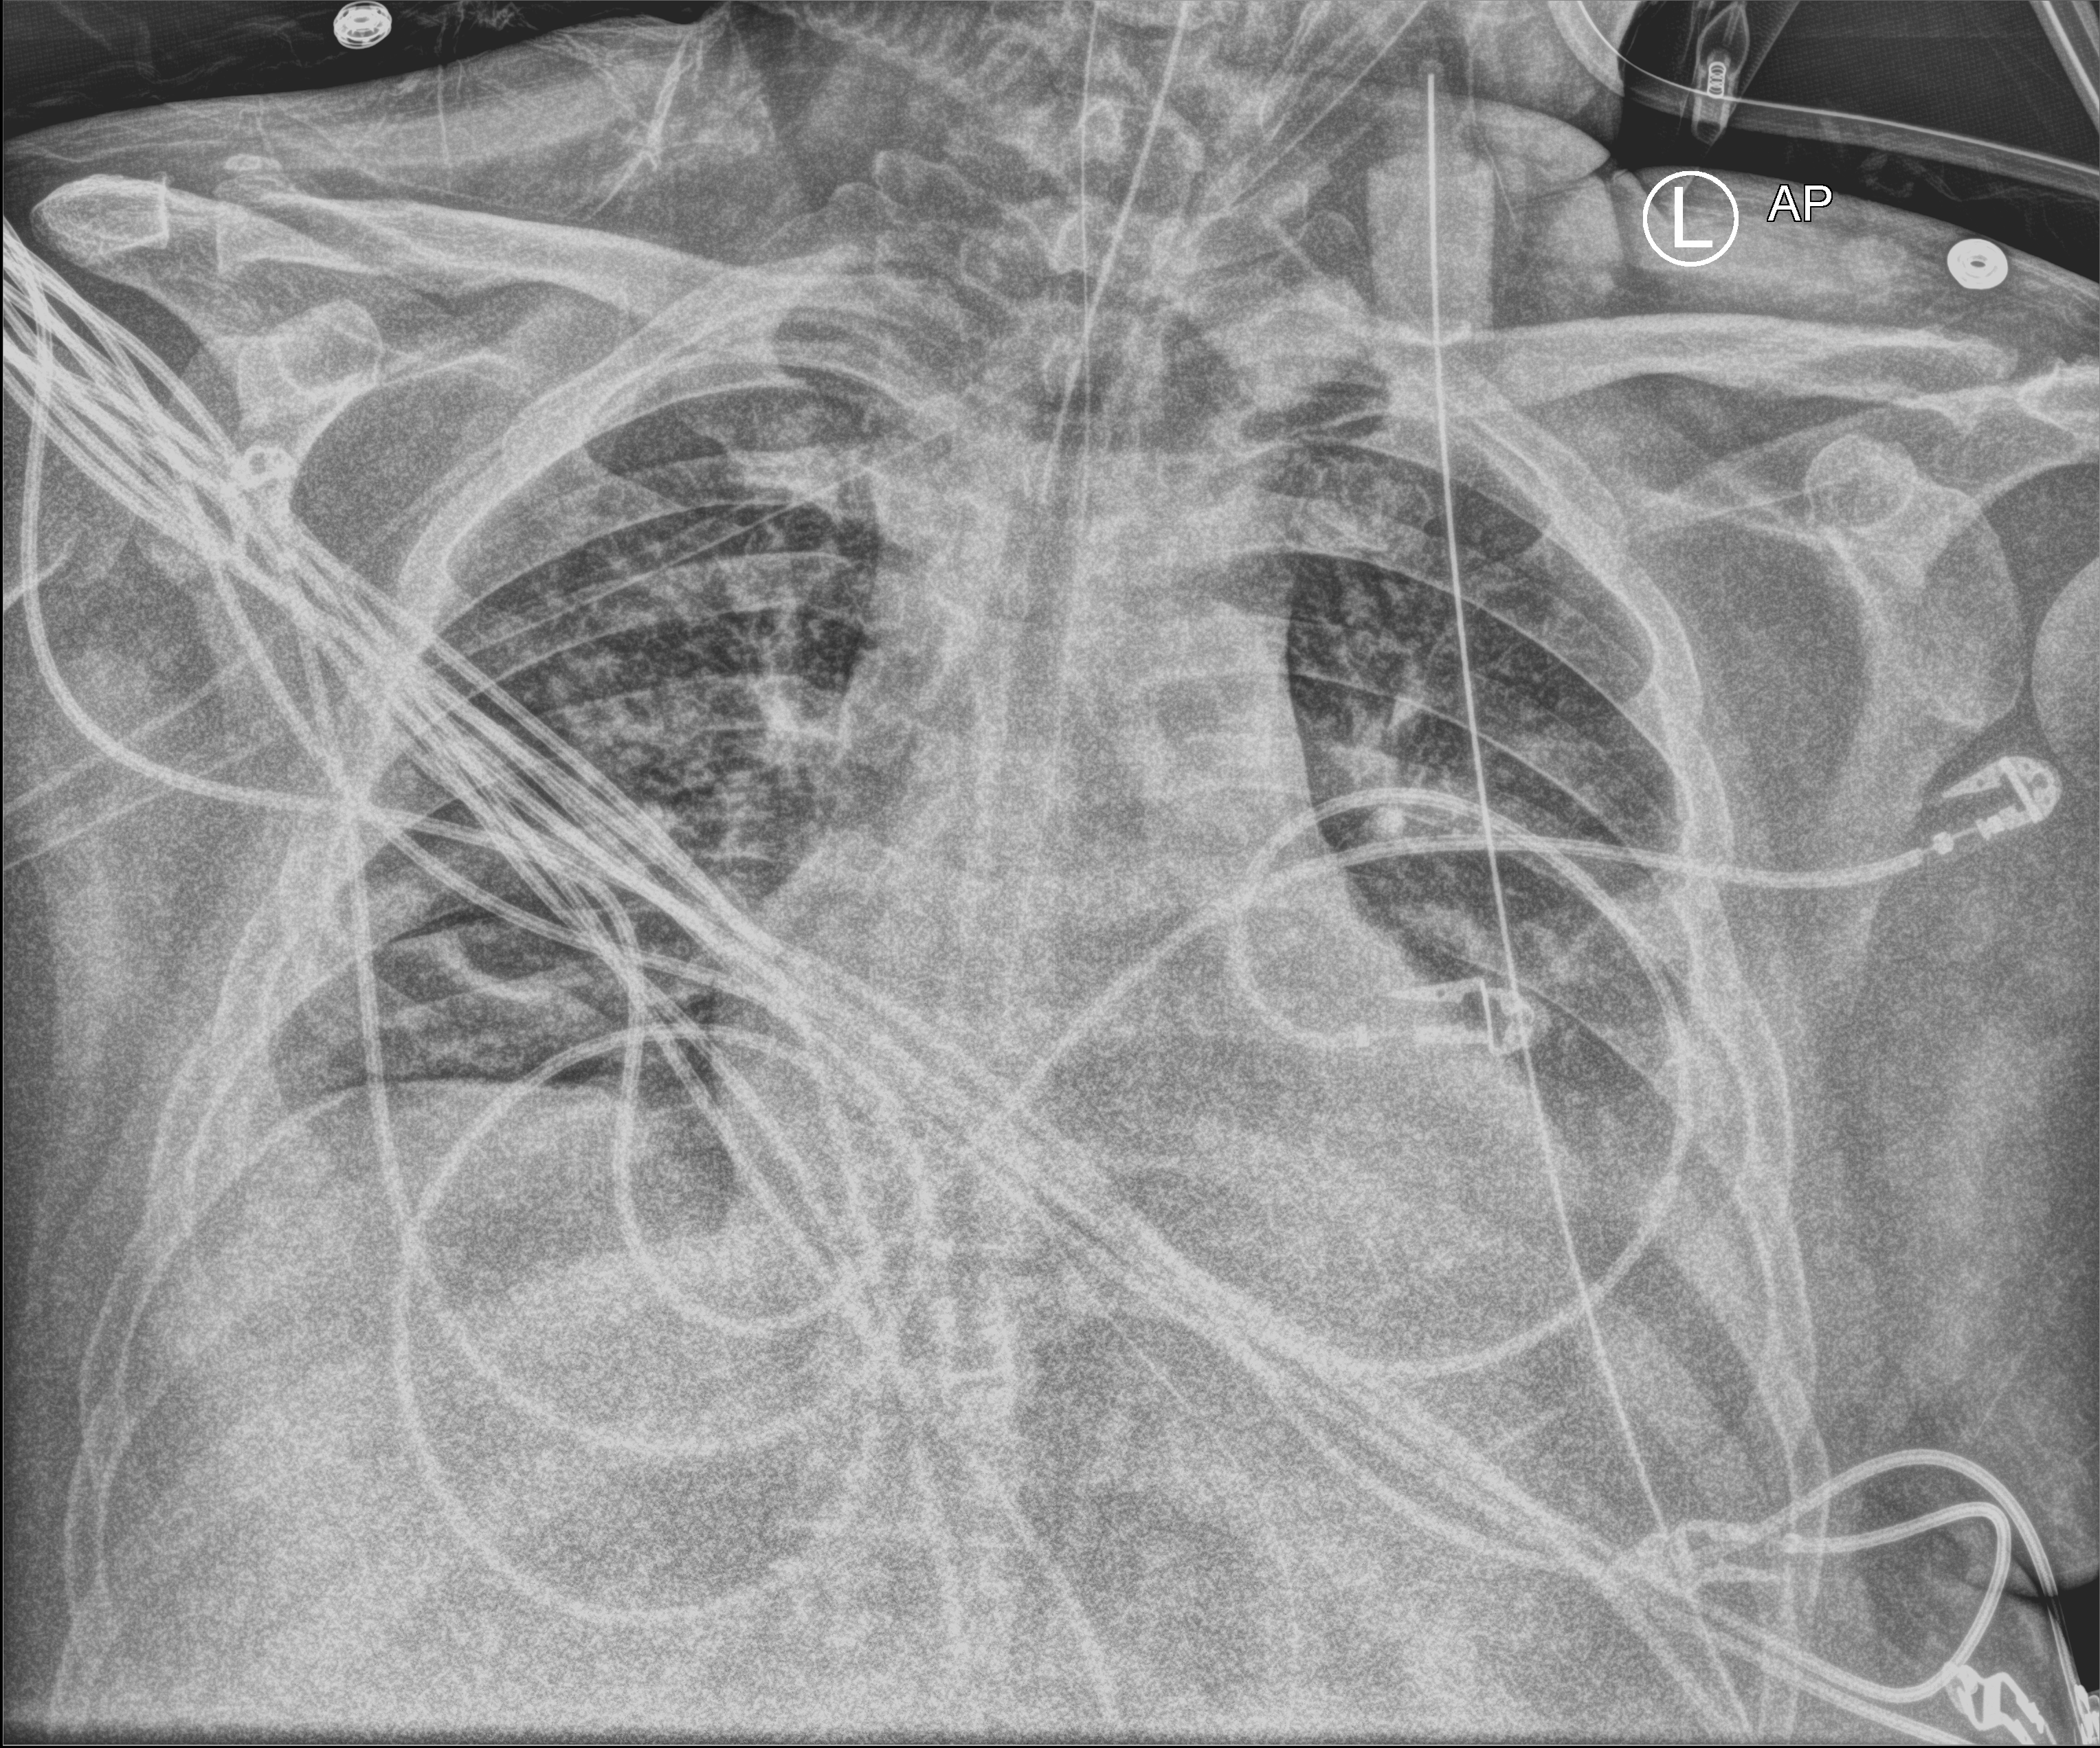
Portable chest radiograph; anteroposterior (AP) projection. Patient hospitalised with COVID-19; male, aged 18–59 years.
From the hospital-stay record, not from the radiograph (when in the stay this image was taken is not recorded):
- admitted to intensive care during this hospital stay: yes